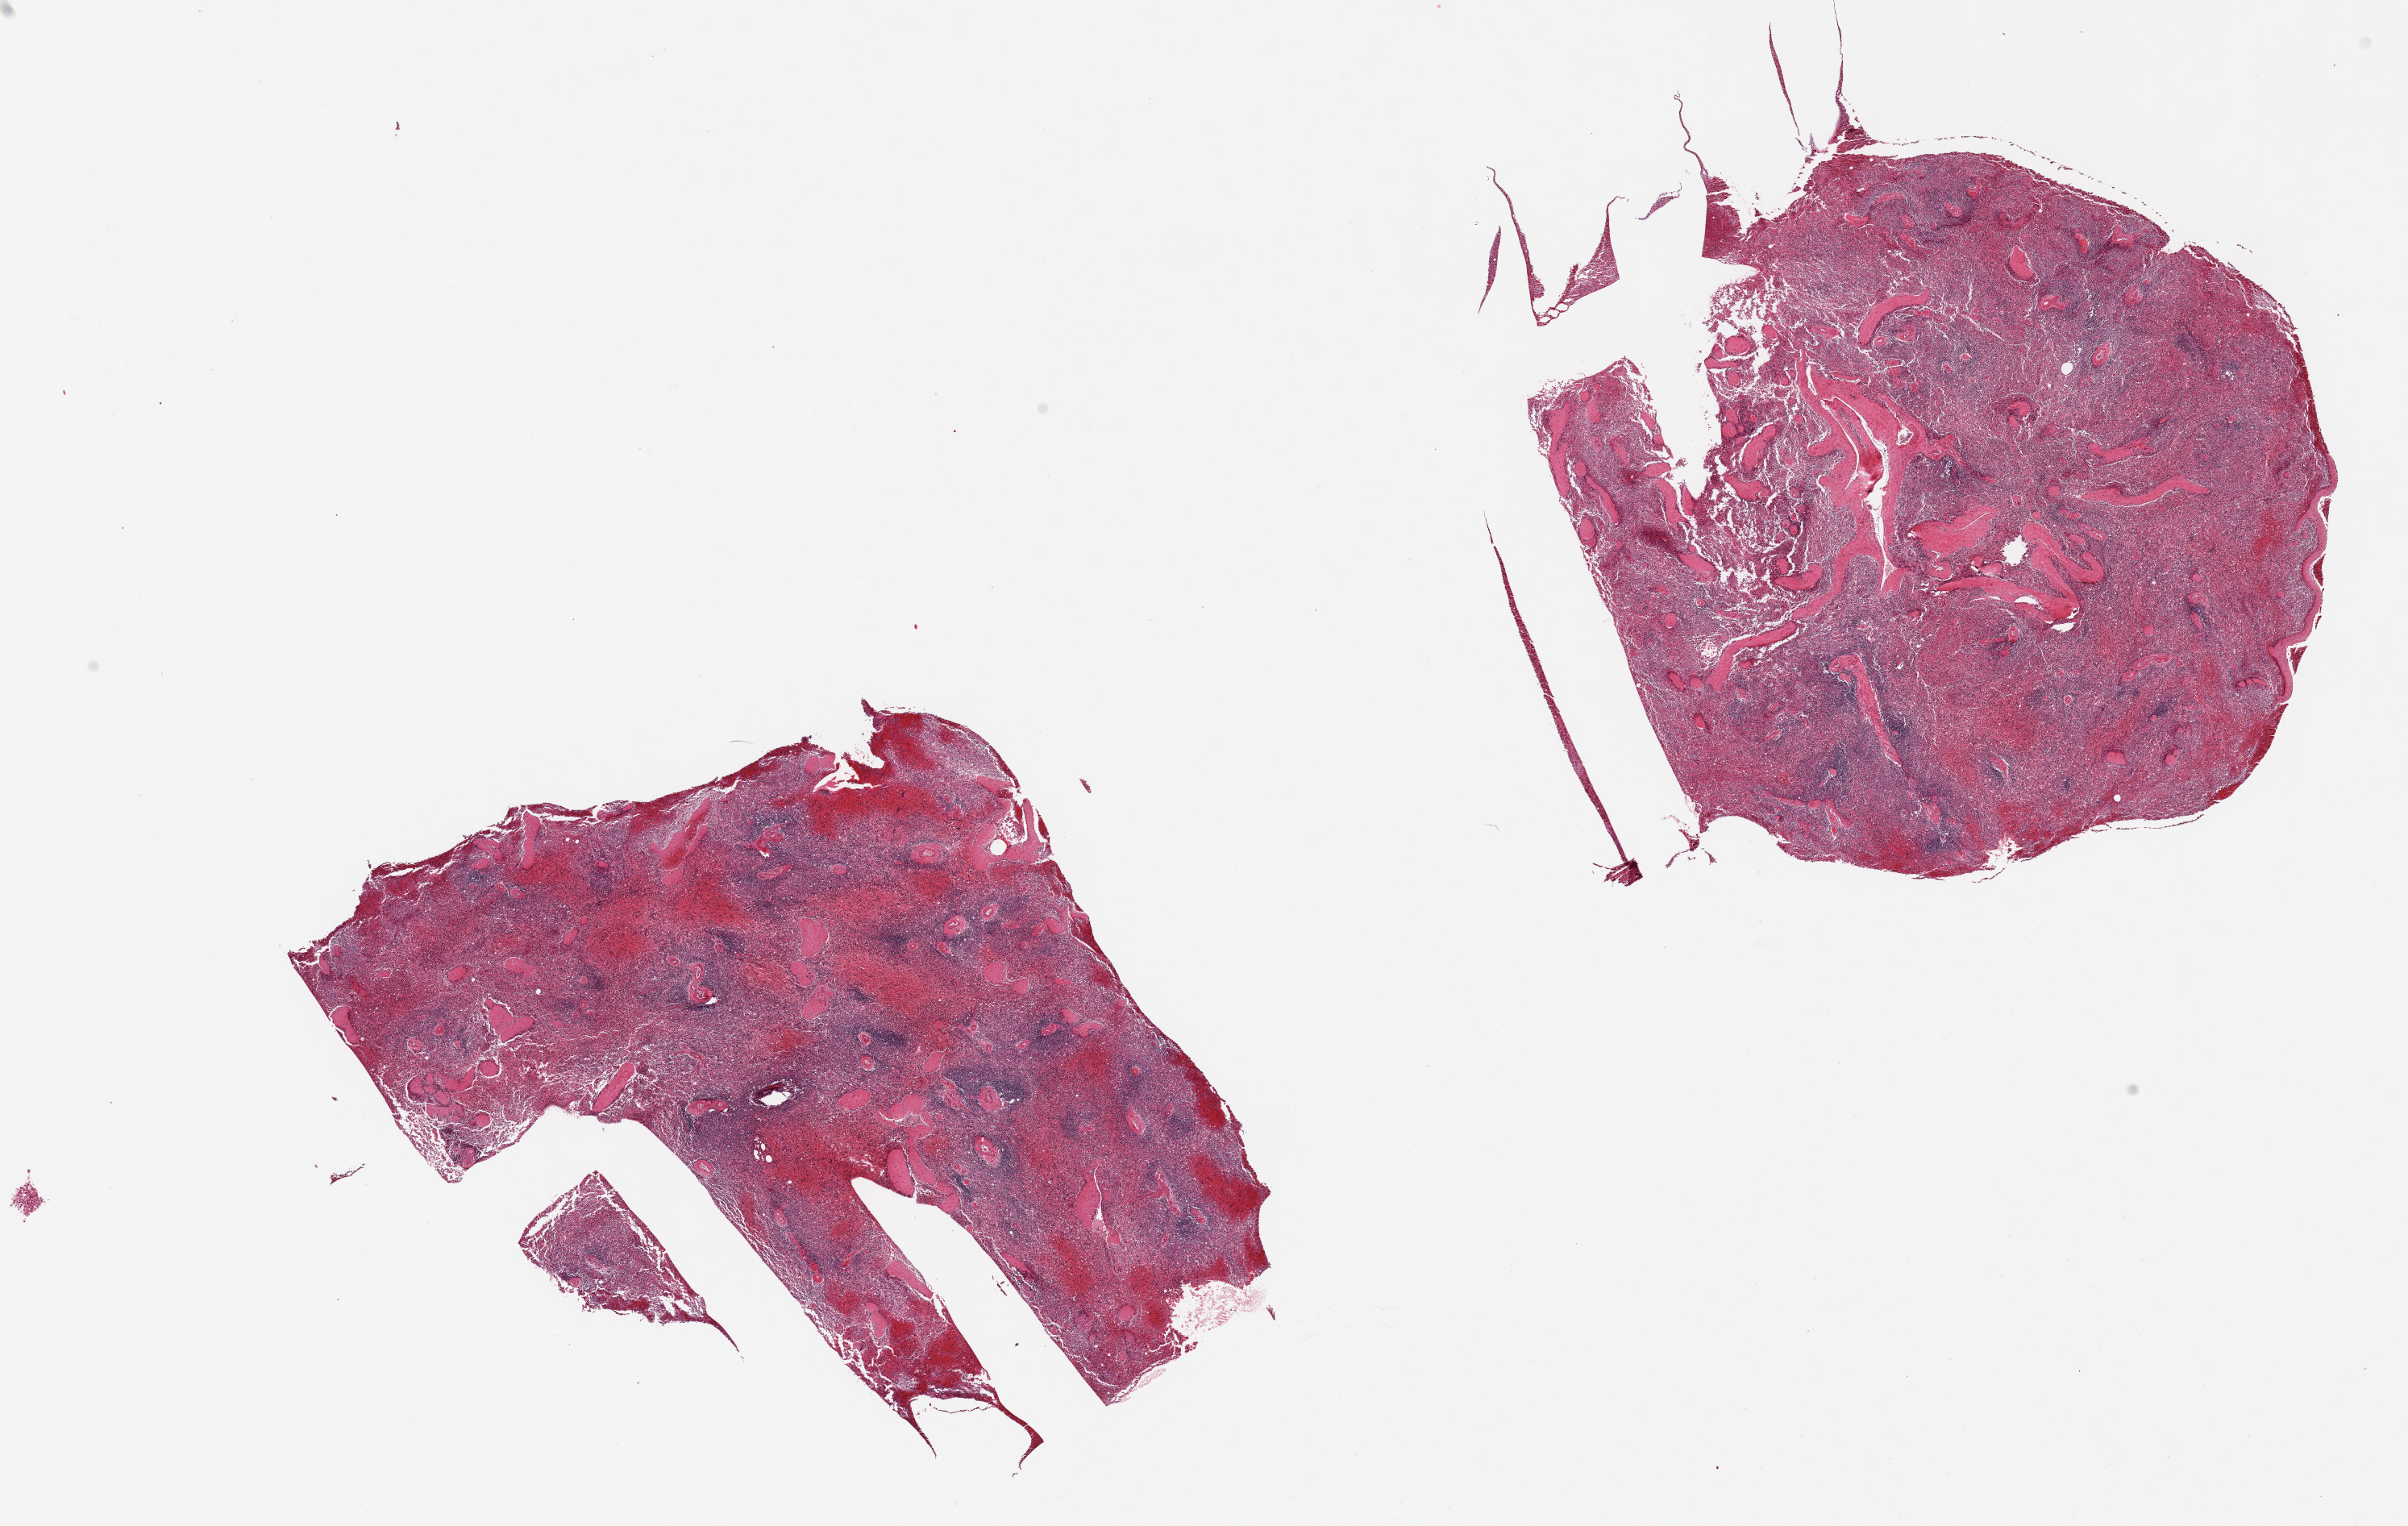
Digitized hematoxylin and eosin (H&E)-stained section — whole scanned area (about 23.6 x 15.0 mm, slide scanned at 20x) shown as a low-resolution overview, PAXgene-fixed paraffin-embedded (PFPE) section, target tissue: spleen, tissue donor sample.
• review note (as recorded): 2 pieces; capsule present in one